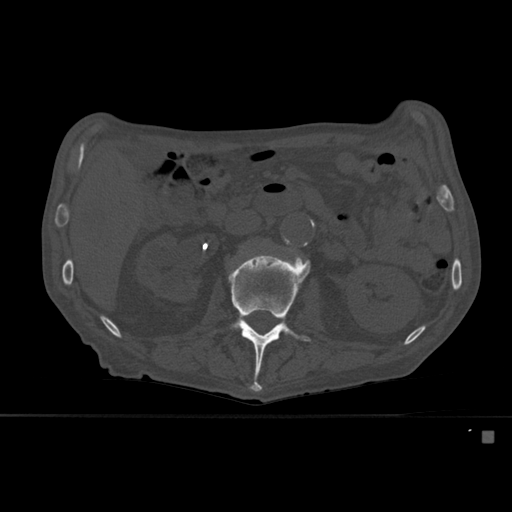
CT including the spine, one axial slice; position 233 of 527 along the scan axis; bone window (W 1800 / L 400 HU); 512 × 512 image matrix. Male patient, age 78 years. Case-level facts recorded for this patient, not image findings: primary cancer: prostate.
Structures marked on this image (semi-automatic segmentation, software-assisted and operator-edited):
- L2 vertebra: bounding box [x1, y1, x2, y2] px = [214, 253, 311, 392]
- L3 vertebra: [285, 238, 307, 246]